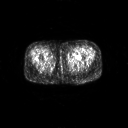
FDG PET of an extremity soft-tissue mass (from a PET/CT study), one axial slice. 128 × 128 image matrix, field of view 700 × 700 mm. Female patient, age 47 years. Case-level facts recorded for this patient, not image findings: histological type: myxofibrosarcoma; grade: intermediate; site of the primary tumour: left thigh.
Outlined on this slice (expert contour drawn on MRI and transferred to this co-registered scan by the dataset authors):
- gross tumour volume including surrounding oedema: box from (x=68, y=53) to (x=81, y=61) px